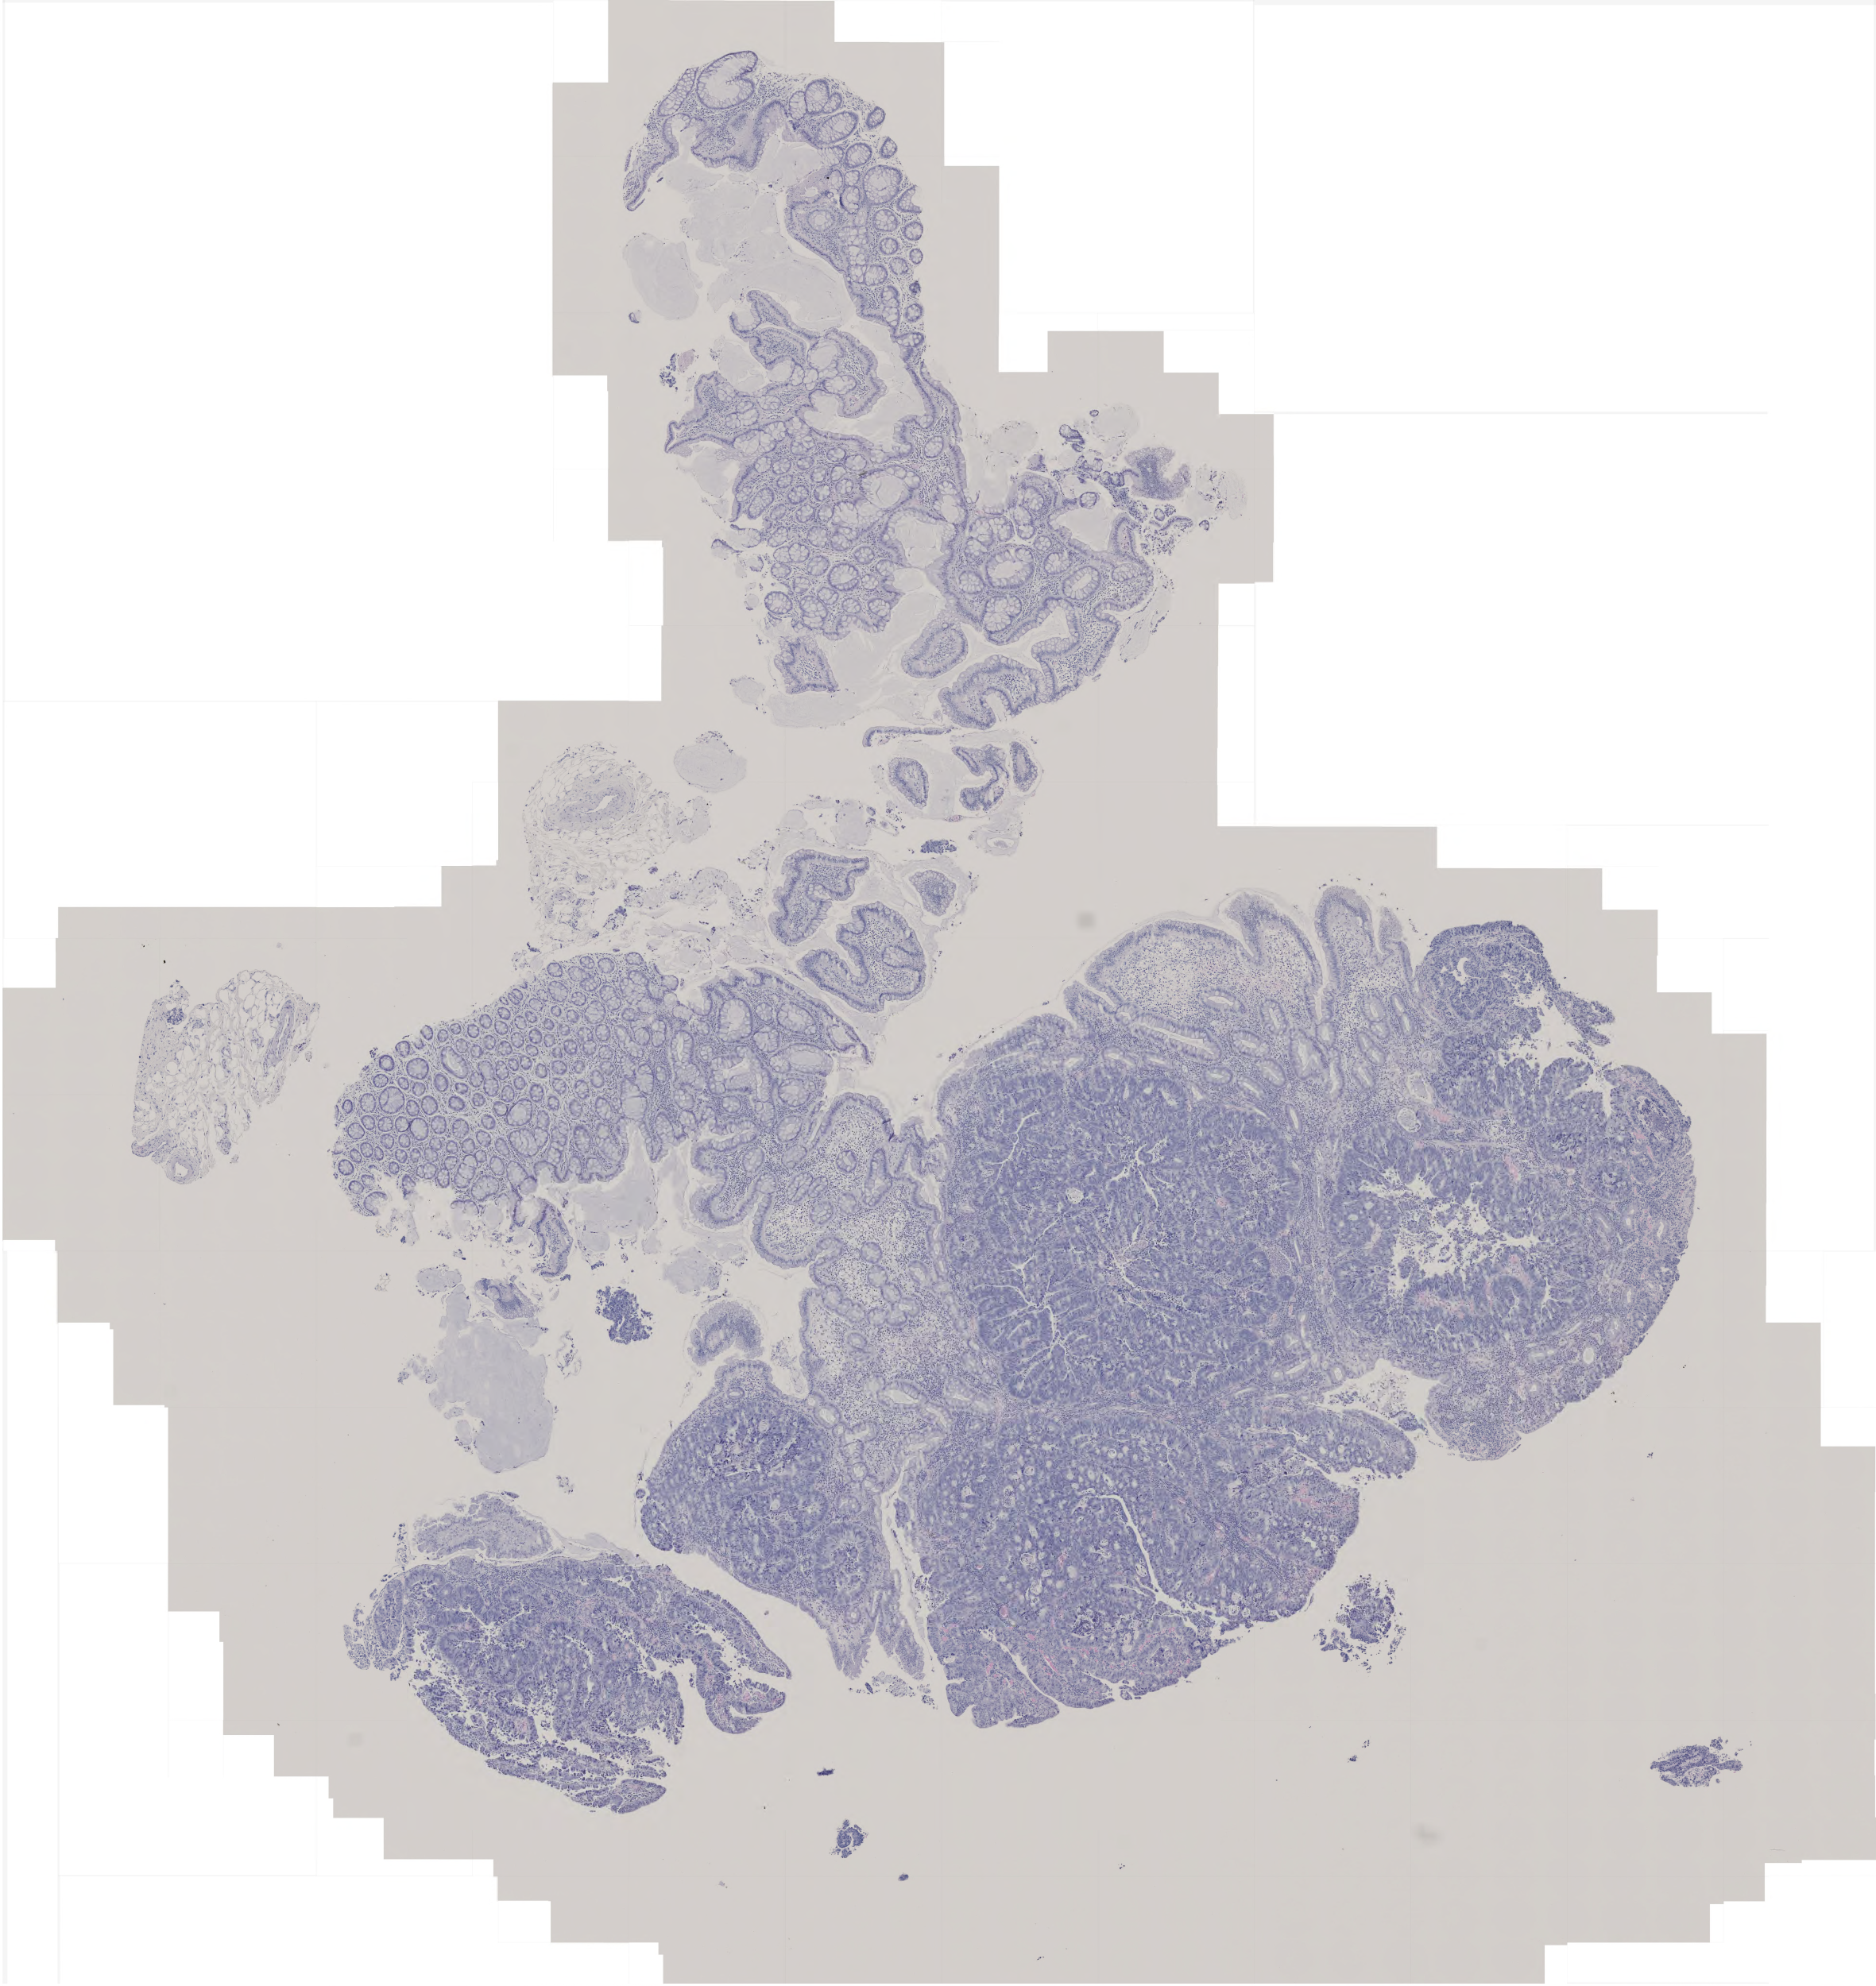
Whole-slide histology image, H&E-stained — whole scanned area (about 4.7 x 5.0 mm) shown as a low-resolution overview, formalin-fixed paraffin-embedded (FFPE) diagnostic section, sample: primary tumour, rectum. Male patient; age at initial diagnosis 83 years.
- TNM: T2 N0 M0
- lymph nodes positive (case pathology): 0 of 16 examined
- AJCC pathologic stage: I (6th edition)
- pathologic diagnosis: Adenocarcinoma, NOS